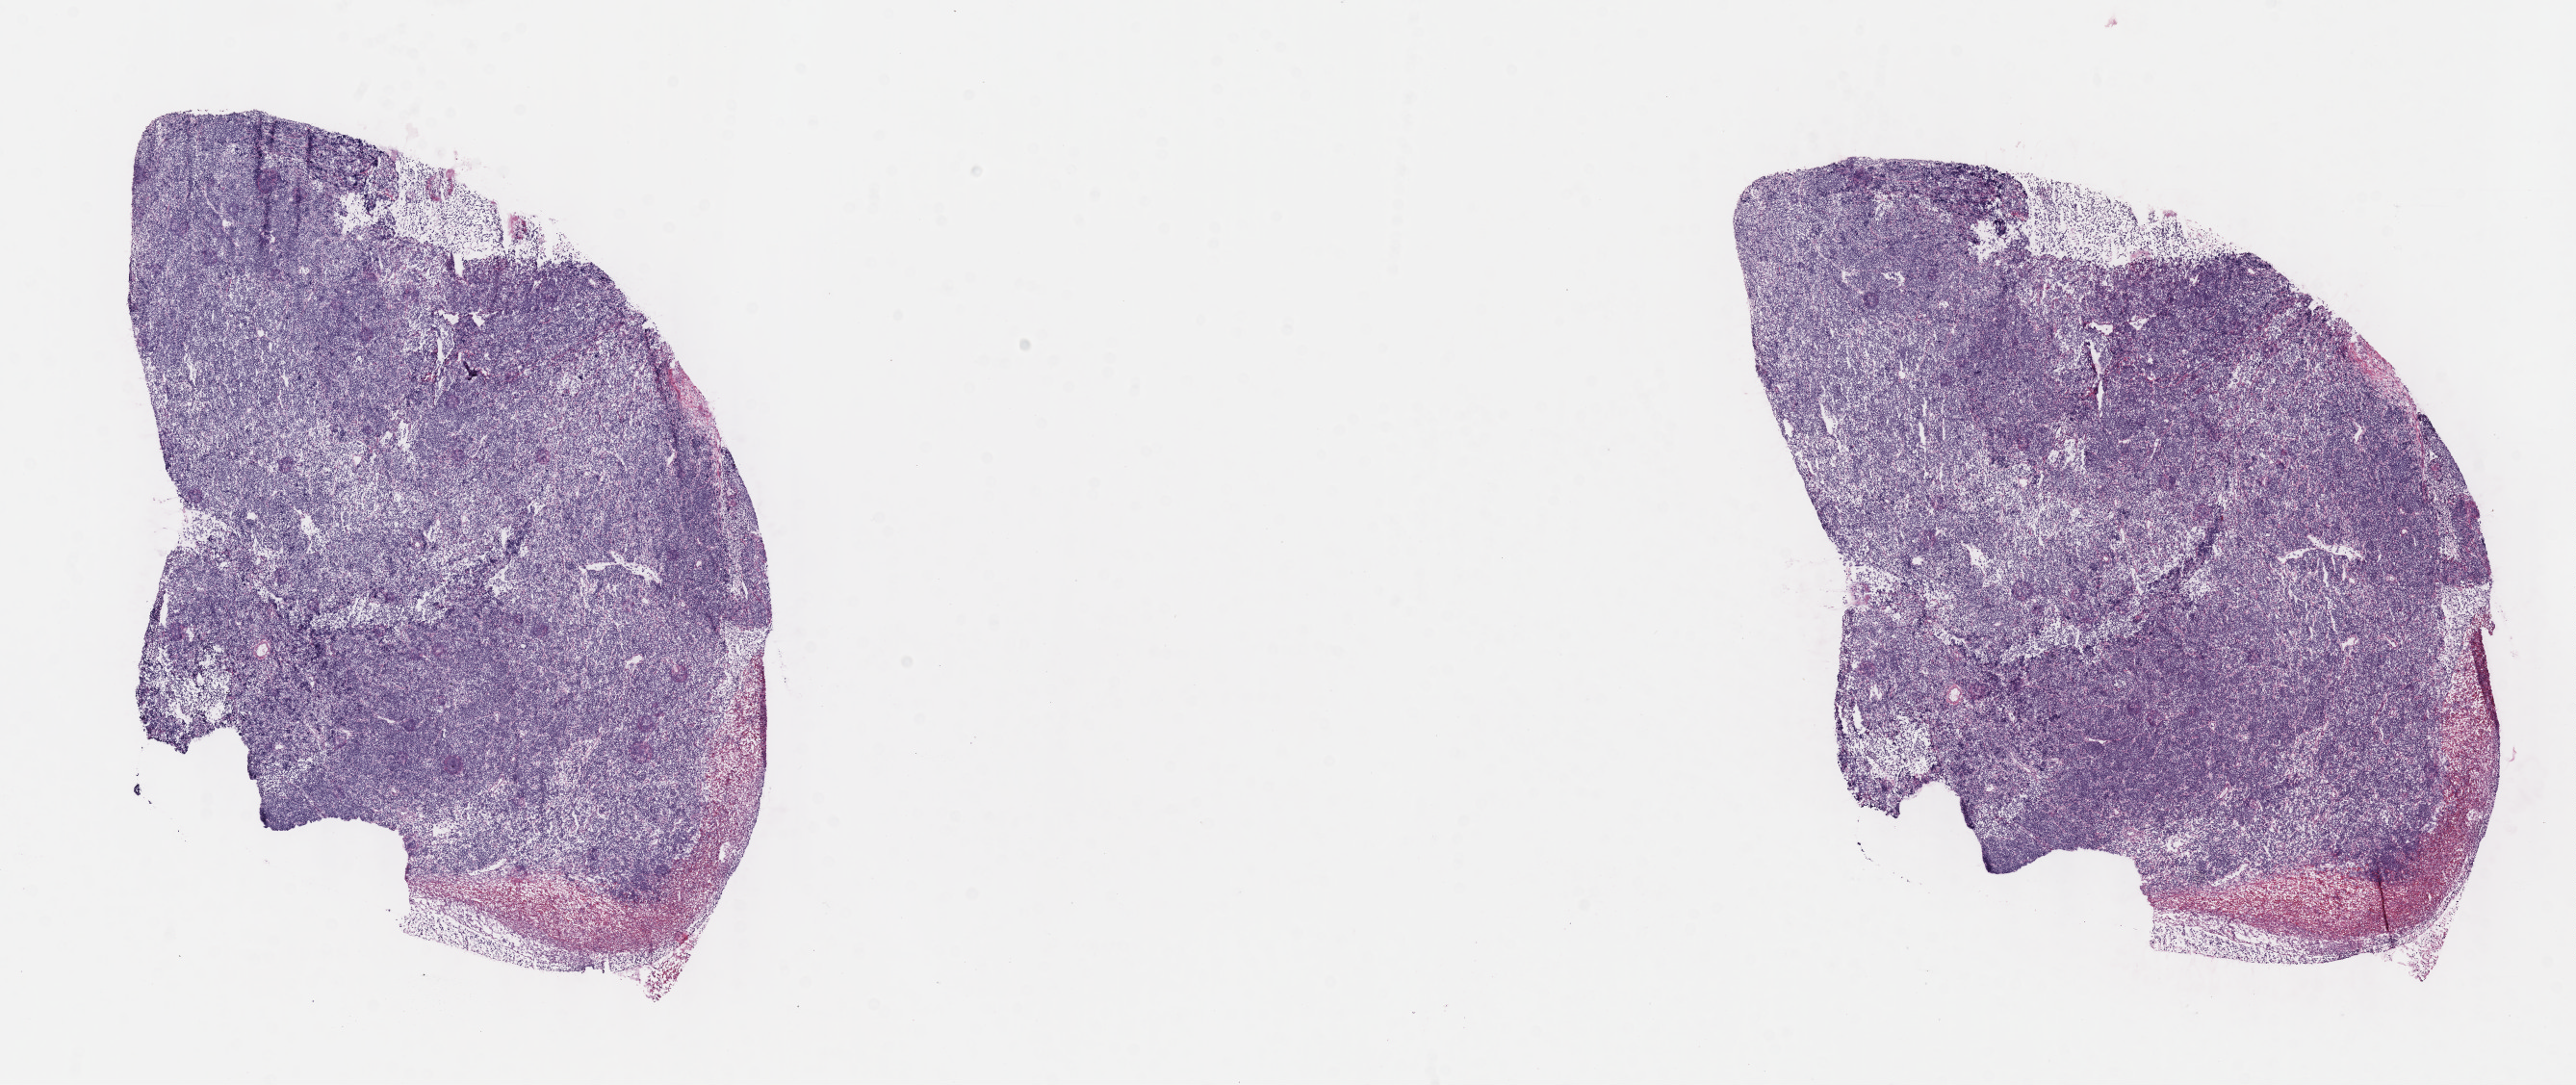
Whole-slide image, hematoxylin and eosin (H&E) stain — a low-resolution overview of the entire scanned area, about 21.6 x 9.1 mm. Cryosection. Specimen: primary tumor. Anatomic site: mandible. Male patient; age at initial diagnosis 6 years. Slide review estimates, as recorded: tumor cells 80%, tumor nuclei 90%, stromal cells 10%, necrosis 10%, normal cells 0%. Infiltration values recorded for this section: lymphocyte infiltration 10%, monocyte infiltration 20%, neutrophil infiltration 10%.
Diagnosis: Burkitt lymphoma, NOS. Ann Arbor stage (patient): Stage IV.